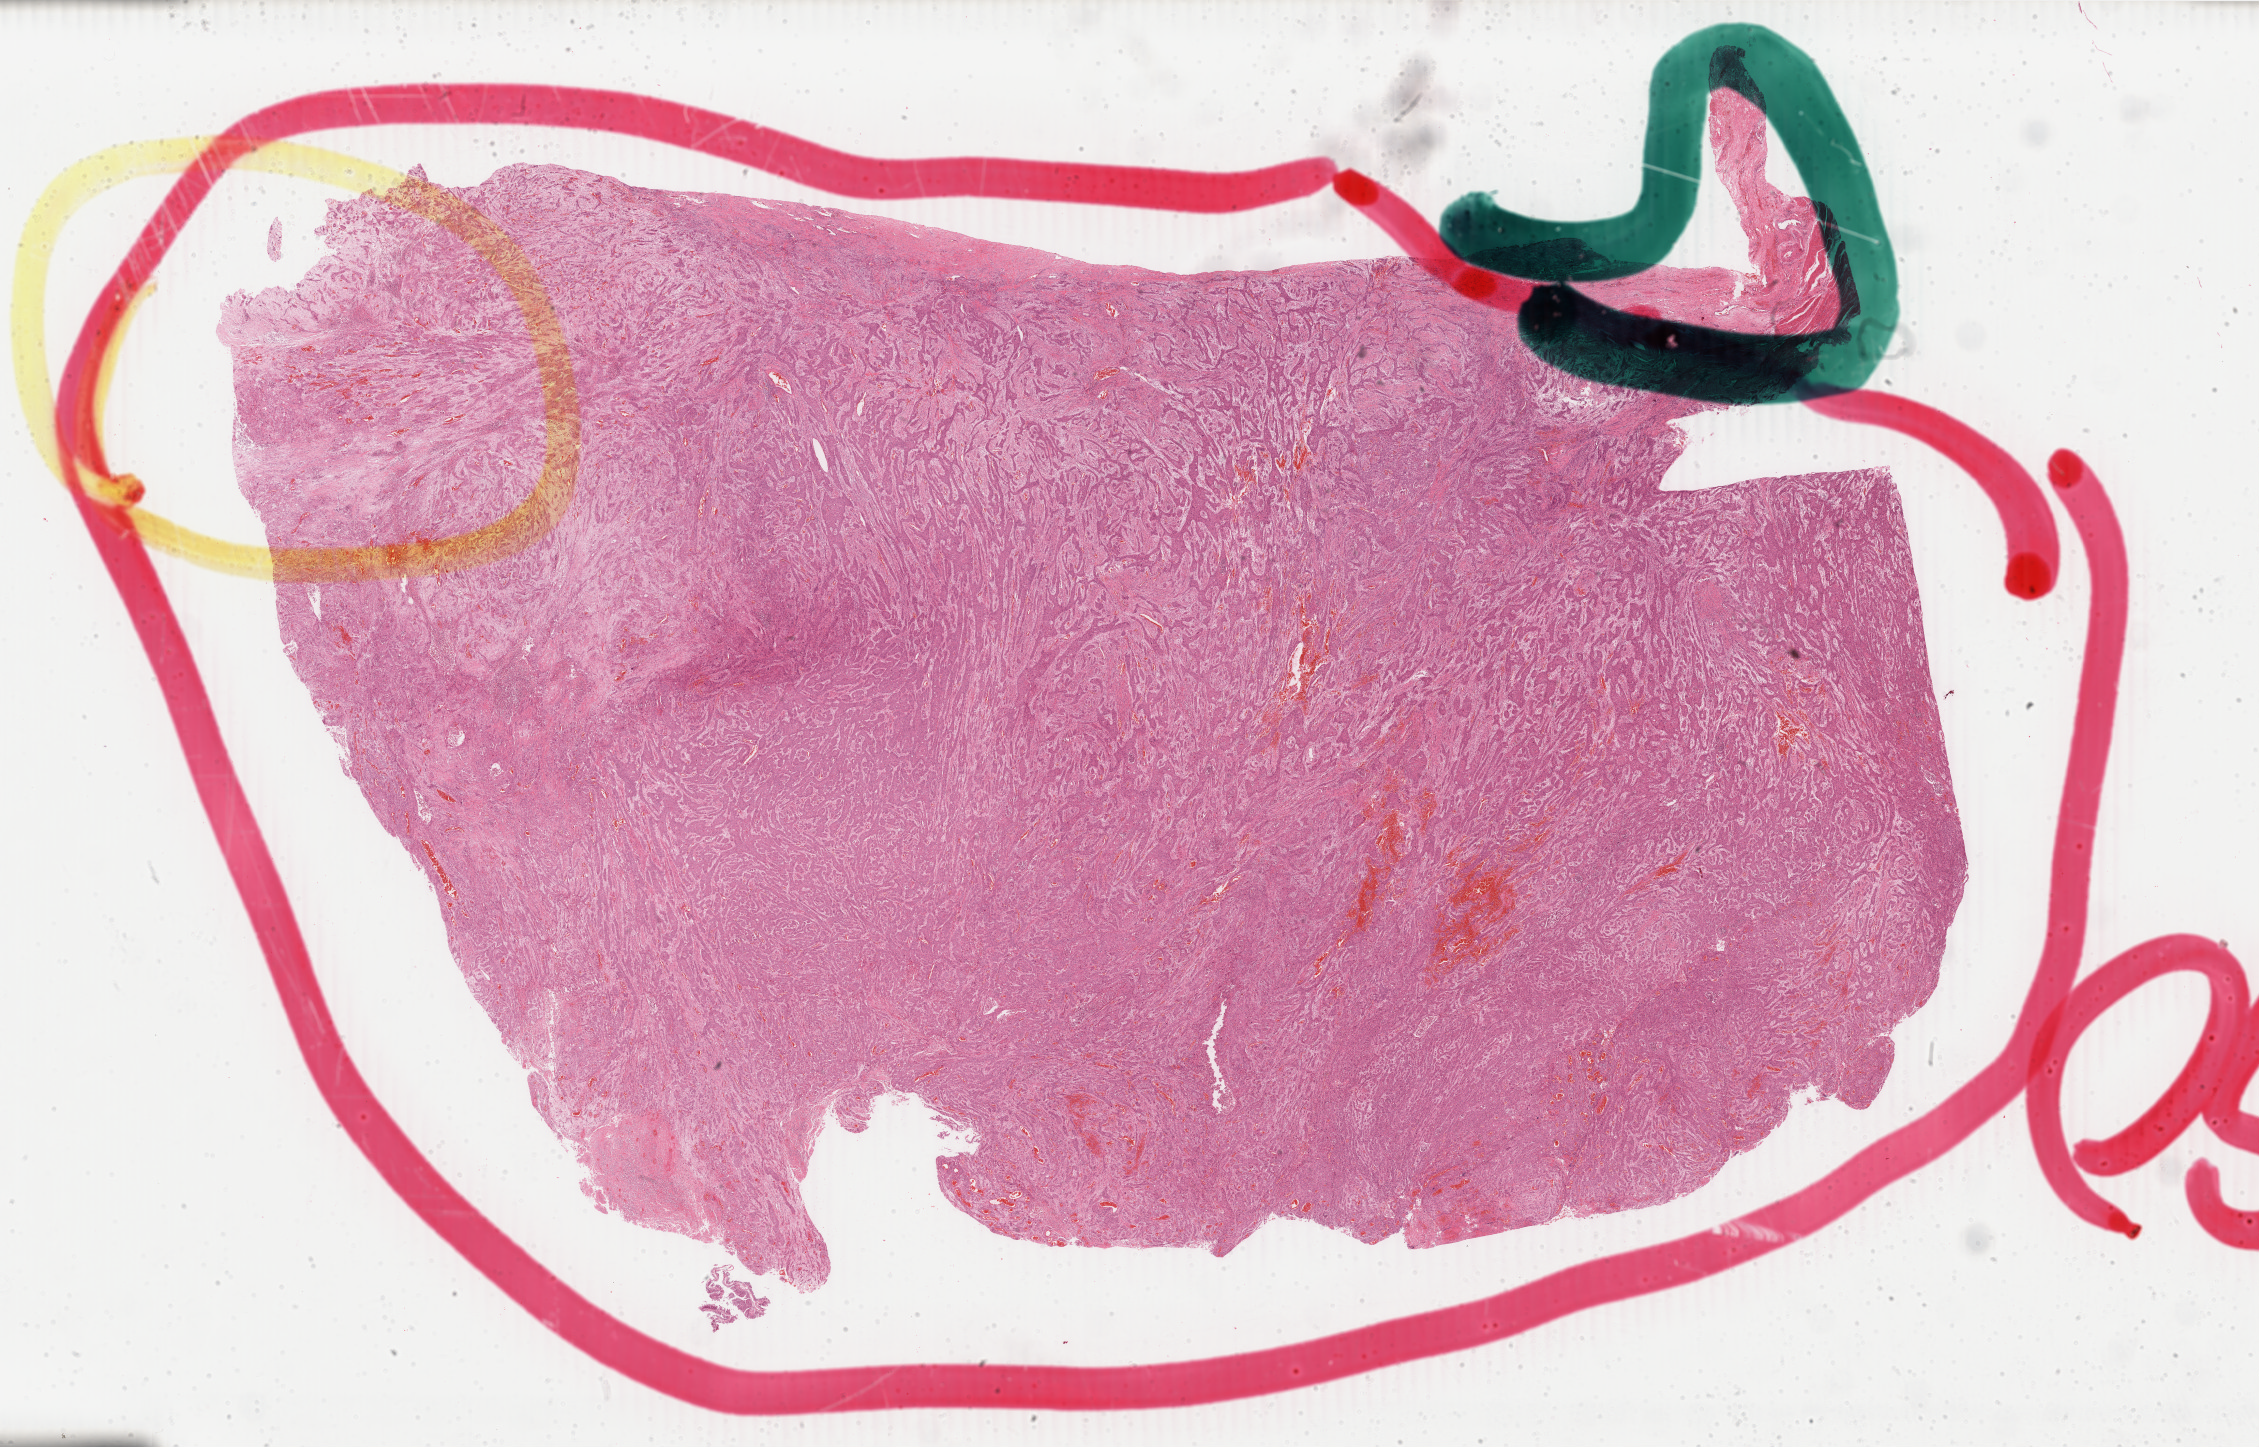
Hematoxylin and eosin (H&E) stained whole-slide image — low-resolution overview of the scanned area, about 35.9 x 23.0 mm. Formalin-fixed paraffin-embedded (FFPE) diagnostic section. Esophagus, primary tumour sample. Male patient; age at initial diagnosis 36 years.
Pathologic diagnosis: Squamous cell carcinoma, NOS (lower third of esophagus).